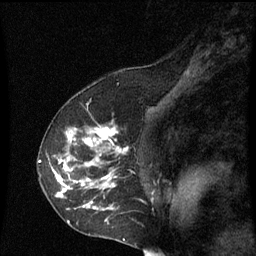
Breast MRI (dynamic contrast-enhanced), one sagittal slice. Slice 42 of 60 in the series (ordered by position). Dynamic contrast-enhanced series, image 2 of 3 at this slice position (ordered by acquisition). 1.5 T. TE 4.2 ms, TR 8.9 ms. 256 × 256 image matrix, field of view 200 × 200 mm. Female patient, age 53 years. Case-level facts recorded for this patient, not image findings: setting: breast cancer imaged before/during neoadjuvant chemotherapy; receptor status: HR-positive, HER2-negative.
Outlined on this slice (semi-automatic segmentation, software-assisted and operator-edited):
- analysis volume of interest (the breast-tissue region the enhancement analysis was run in; not a lesion): bounding box [x1, y1, x2, y2] px = [38, 128, 129, 227]
- tumour enhancement mask (voxels above the 70 % enhancement threshold inside the analysis volume of interest): [52, 128, 125, 209]